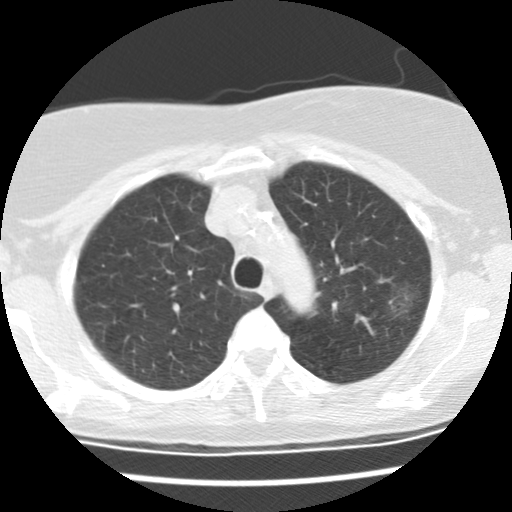
Chest CT (low-dose screening protocol), one axial image, baseline screening round, lung window (W 1500 / L -600 HU), 2.5 mm slice thickness, 120 kVp, slice 109 of 137 in the series, 512 × 512 image matrix. Female participant, aged 66 years at enrolment. Former smoker at enrolment.
• Expert reader's lesion annotation, bounding box [x1, y1, x2, y2] px = [381, 278, 425, 323].
• Reader record for this screening exam (exam-level; its link to the box is not recorded): non-calcified nodule or mass ≥4 mm, left upper lobe, 25 × 17 mm, poorly defined margins, mixed attenuation.
• Official screen result: positive, change unspecified: nodule(s) >= 4 mm or enlarging nodule(s), mass(es), or other non-specific abnormalities suspicious for lung cancer.